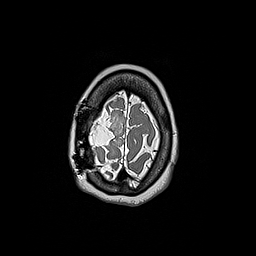
Brain MRI from a brain-tumour surgery series, one axial slice. Slice 41 of 192 in the series (ordered by position). 1 mm slice thickness. 256 × 256 image matrix, field of view 250 × 250 mm. From the clinical record (not read from this slice): histopathology: Oligodendroglioma; WHO grade: 3; IDH mutation: yes.
Annotated regions visible in this slice (outlined manually by an expert reader):
- tumour: bounding box [x1, y1, x2, y2] px = [89, 139, 94, 148]